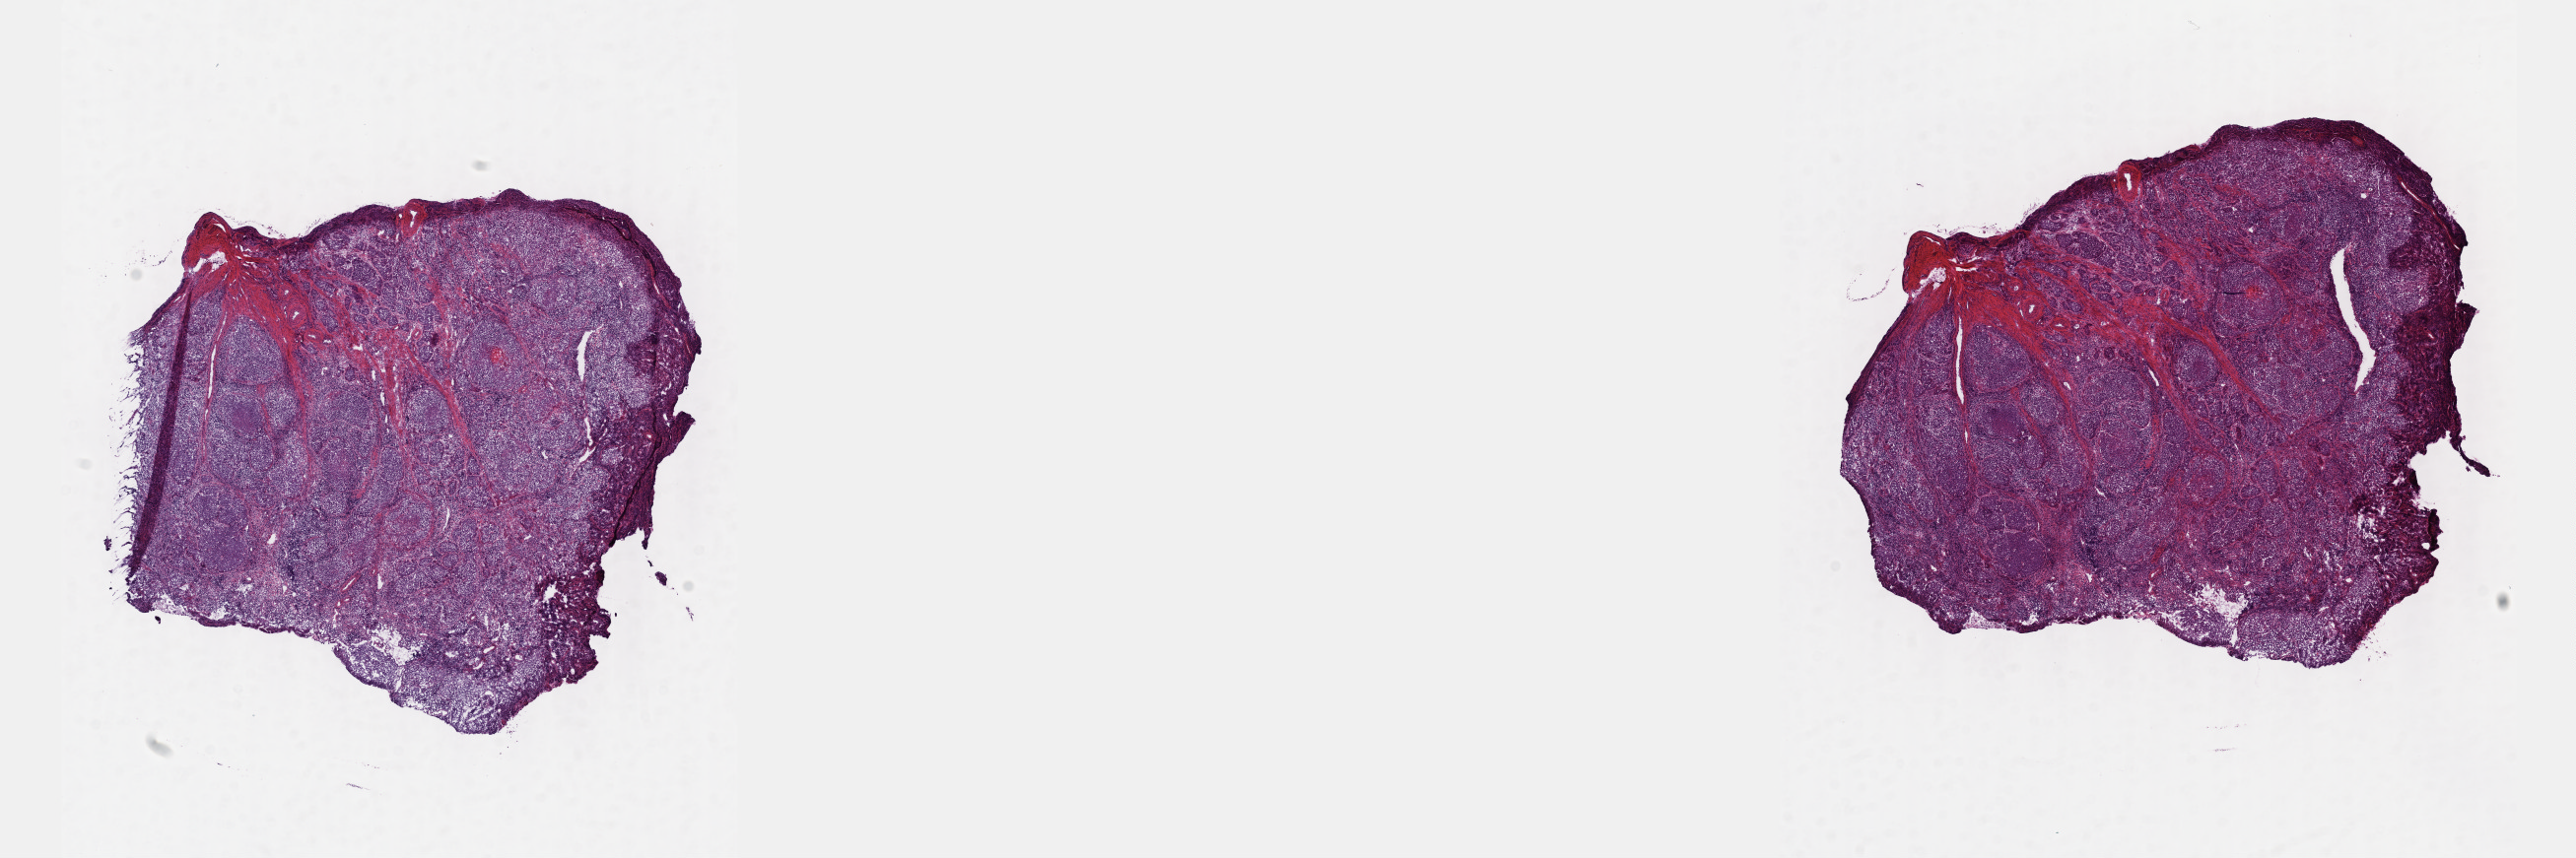
H&E whole-slide image, whole scanned area (about 21.1 x 7.0 mm) shown as a low-resolution overview; frozen section from the top of the tissue portion; primary tumour sample from the cervix. Female, age 29 years at initial diagnosis. Histologic grade: G2 (moderately differentiated). Slide review estimates, as recorded: tumour cells 100%, tumour nuclei 80%, normal cells 0%, stromal cells 0%, necrosis 0%. Infiltration values recorded for this section: lymphocyte infiltration 2%, monocyte infiltration 0%, neutrophil infiltration 0%.
Pathologic diagnosis: Squamous cell carcinoma, NOS. FIGO stage: IB1. Lymph nodes positive (case pathology): 0 of 26 examined.